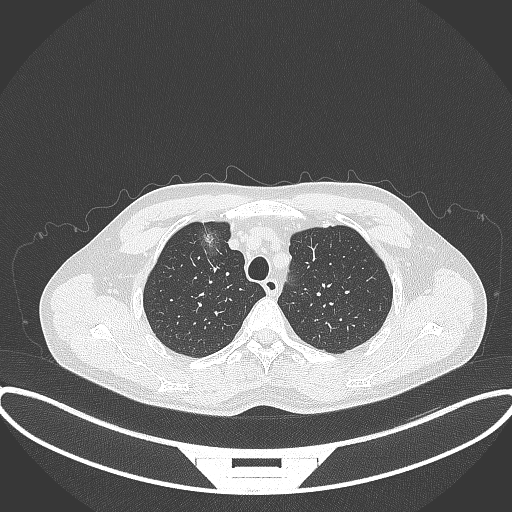
Chest CT, one axial slice. Slice 295 of 395 in the series (ordered by position). Reconstruction kernel B70f. 120 kVp. Lung window (W 1500 / L -600 HU). 512 × 512 image matrix, field of view 424 × 424 mm. Patient: male, 60 years. From the clinical record (not read from this slice): clinical TNM (as recorded): T1c N0 M0.
Outlined on this slice (rectangle marked by the reading radiologist):
- lung tumour (recorded histology: adenocarcinoma): bounding box <189,217,230,260> (left, top, right, bottom; pixels)